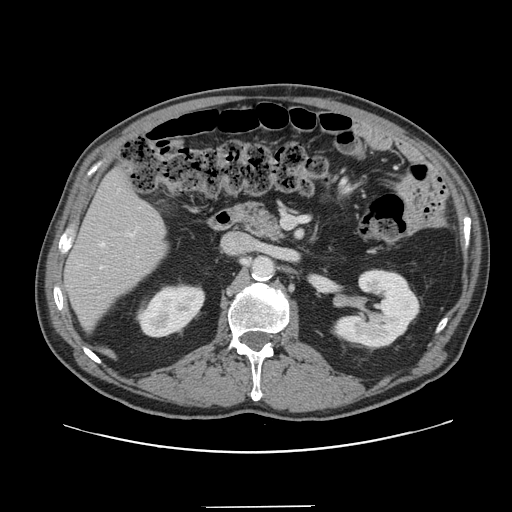
Contrast-enhanced abdominal CT, one axial slice; position 68 of 139 along the scan axis; 120 kVp; soft-tissue window (W 400 / L 40 HU); 2.5 mm slice thickness; 512 × 512 image matrix. Male patient, age 64 years. From the clinical record (not read from this slice): diagnosis: colorectal cancer liver metastases, imaged before liver resection; multiple liver metastases: yes; largest metastasis: 3.5 cm; disease in both lobes: yes.
Annotated regions visible in this slice (outlined manually by an expert reader):
- hepatic veins: box from (x=100, y=243) to (x=105, y=269) px
- liver: (x=66, y=172)–(x=164, y=326)
- planned liver remnant (the part of the liver to remain after resection): (x=66, y=172)–(x=165, y=327)
- portal vein (with intrahepatic branches): (x=128, y=233)–(x=133, y=236)